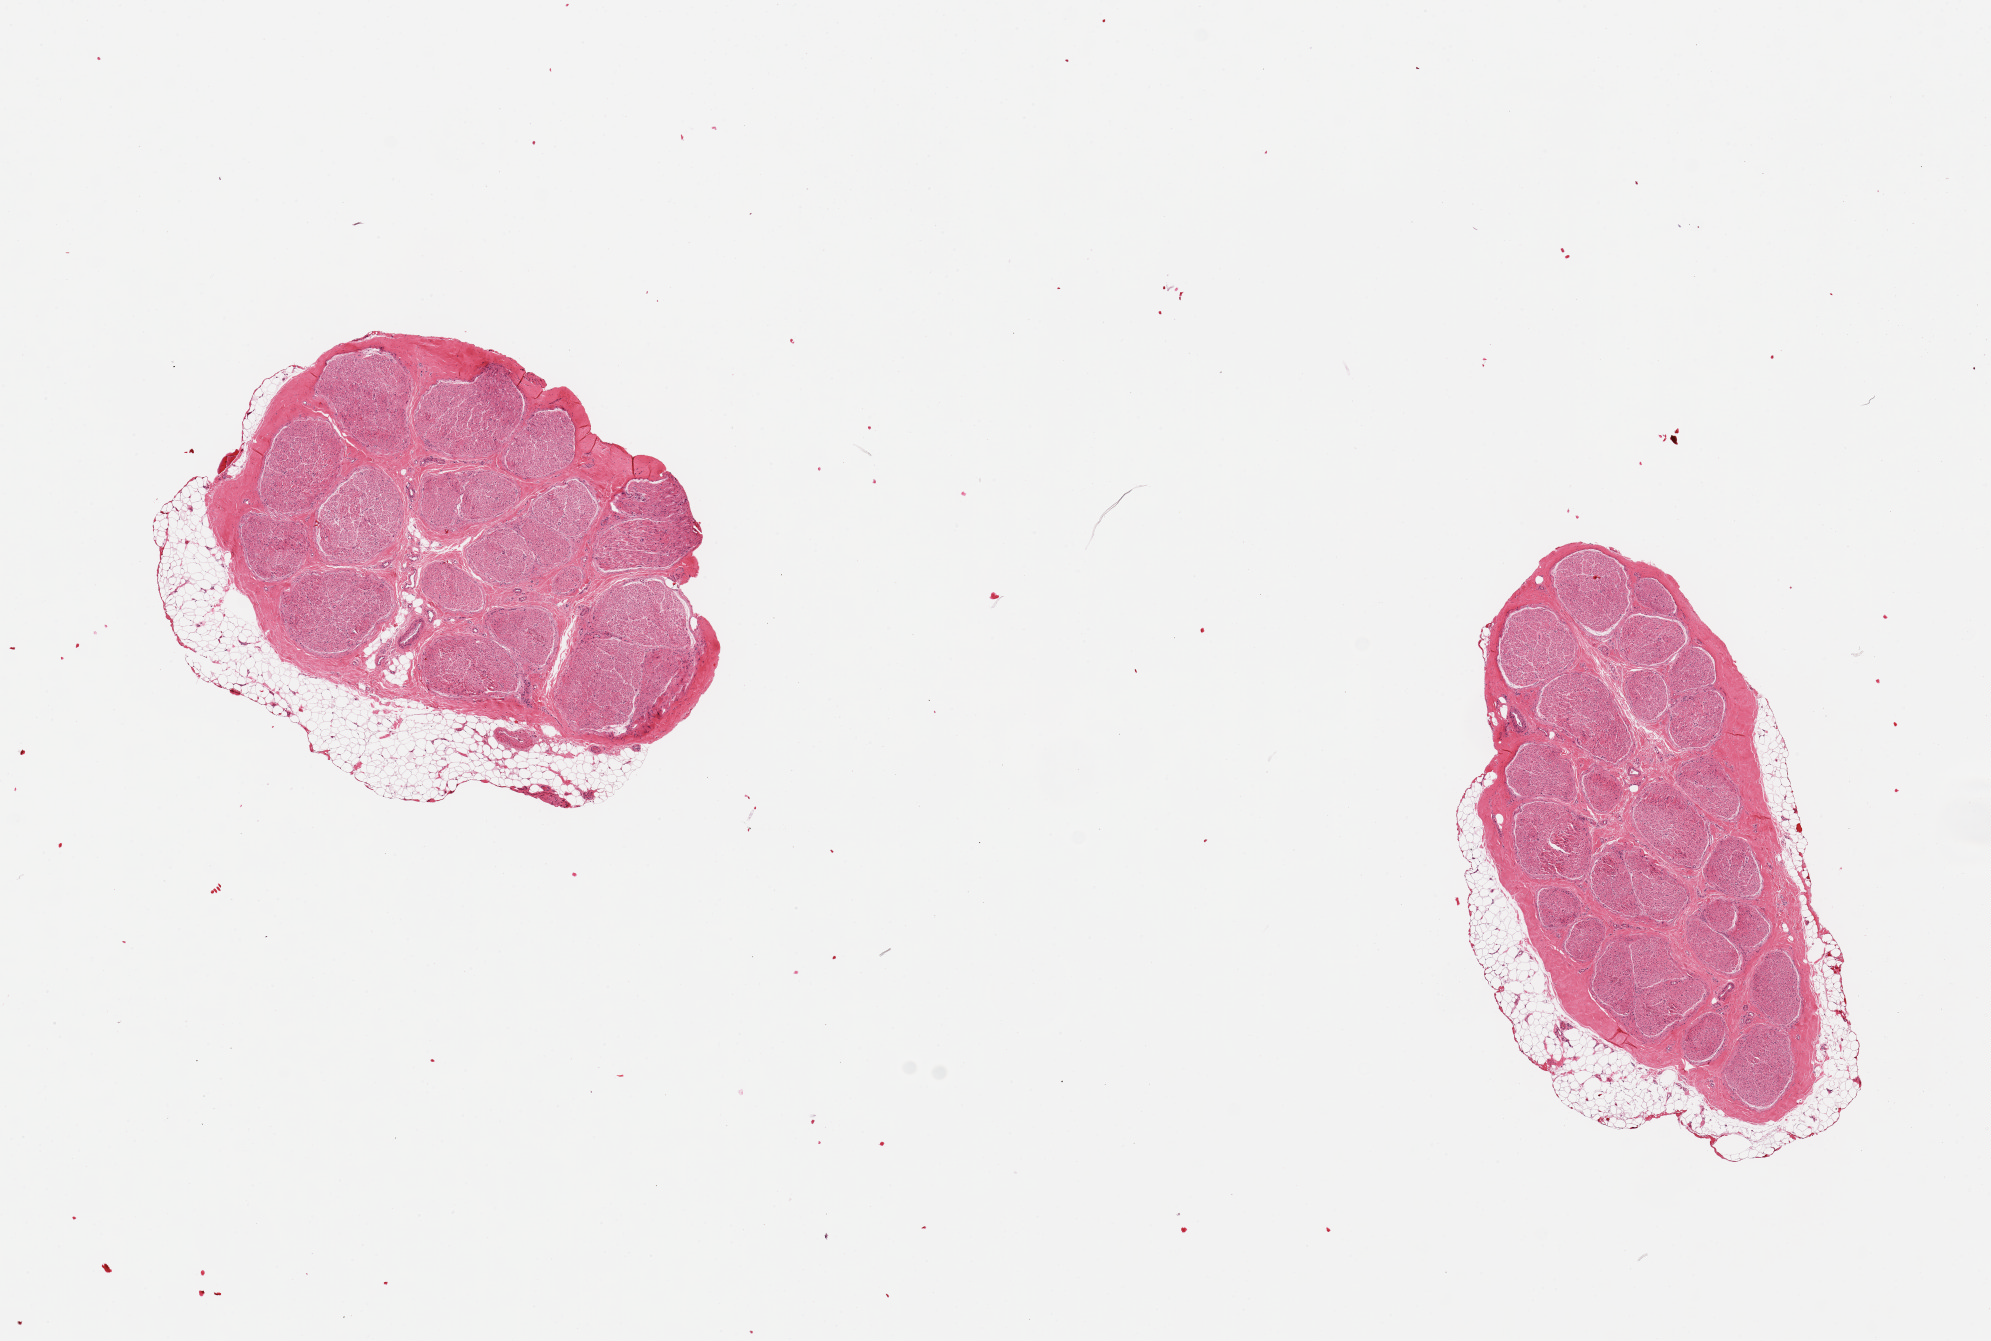
Digitized haematoxylin and eosin-stained section, whole scanned area (about 15.8 x 10.6 mm, slide scanned at 20x) shown as a low-resolution overview, PAXgene-fixed paraffin-embedded (PFPE) section, target tissue: tibial nerve, tissue donor sample. Donor: male.
• pathologist's review note for this sample: 2 pieces, partial rims of adherent fat, ~0.5mm; fairly good specimens